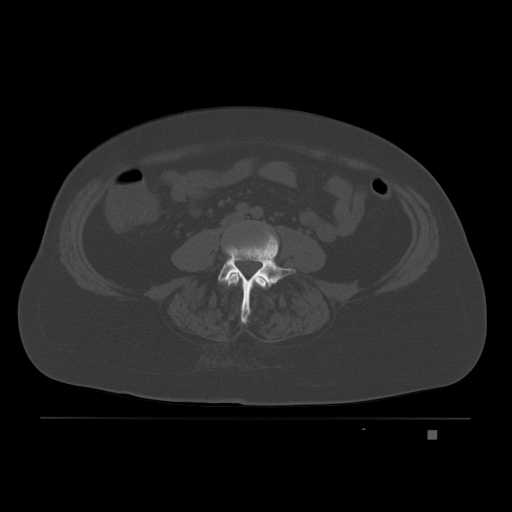
CT including the spine, one axial slice. Position 43 of 221 along the scan axis. Bone window (W 1800 / L 400 HU). 512 × 512 image matrix. Female patient, age 63 years. Case-level facts recorded for this patient, not image findings: primary cancer: breast.
Structures marked on this image (semi-automatic segmentation, software-assisted and operator-edited):
- L3 vertebra: bounding box [x1, y1, x2, y2] px = [227, 272, 270, 289]
- L4 vertebra: [218, 230, 296, 323]